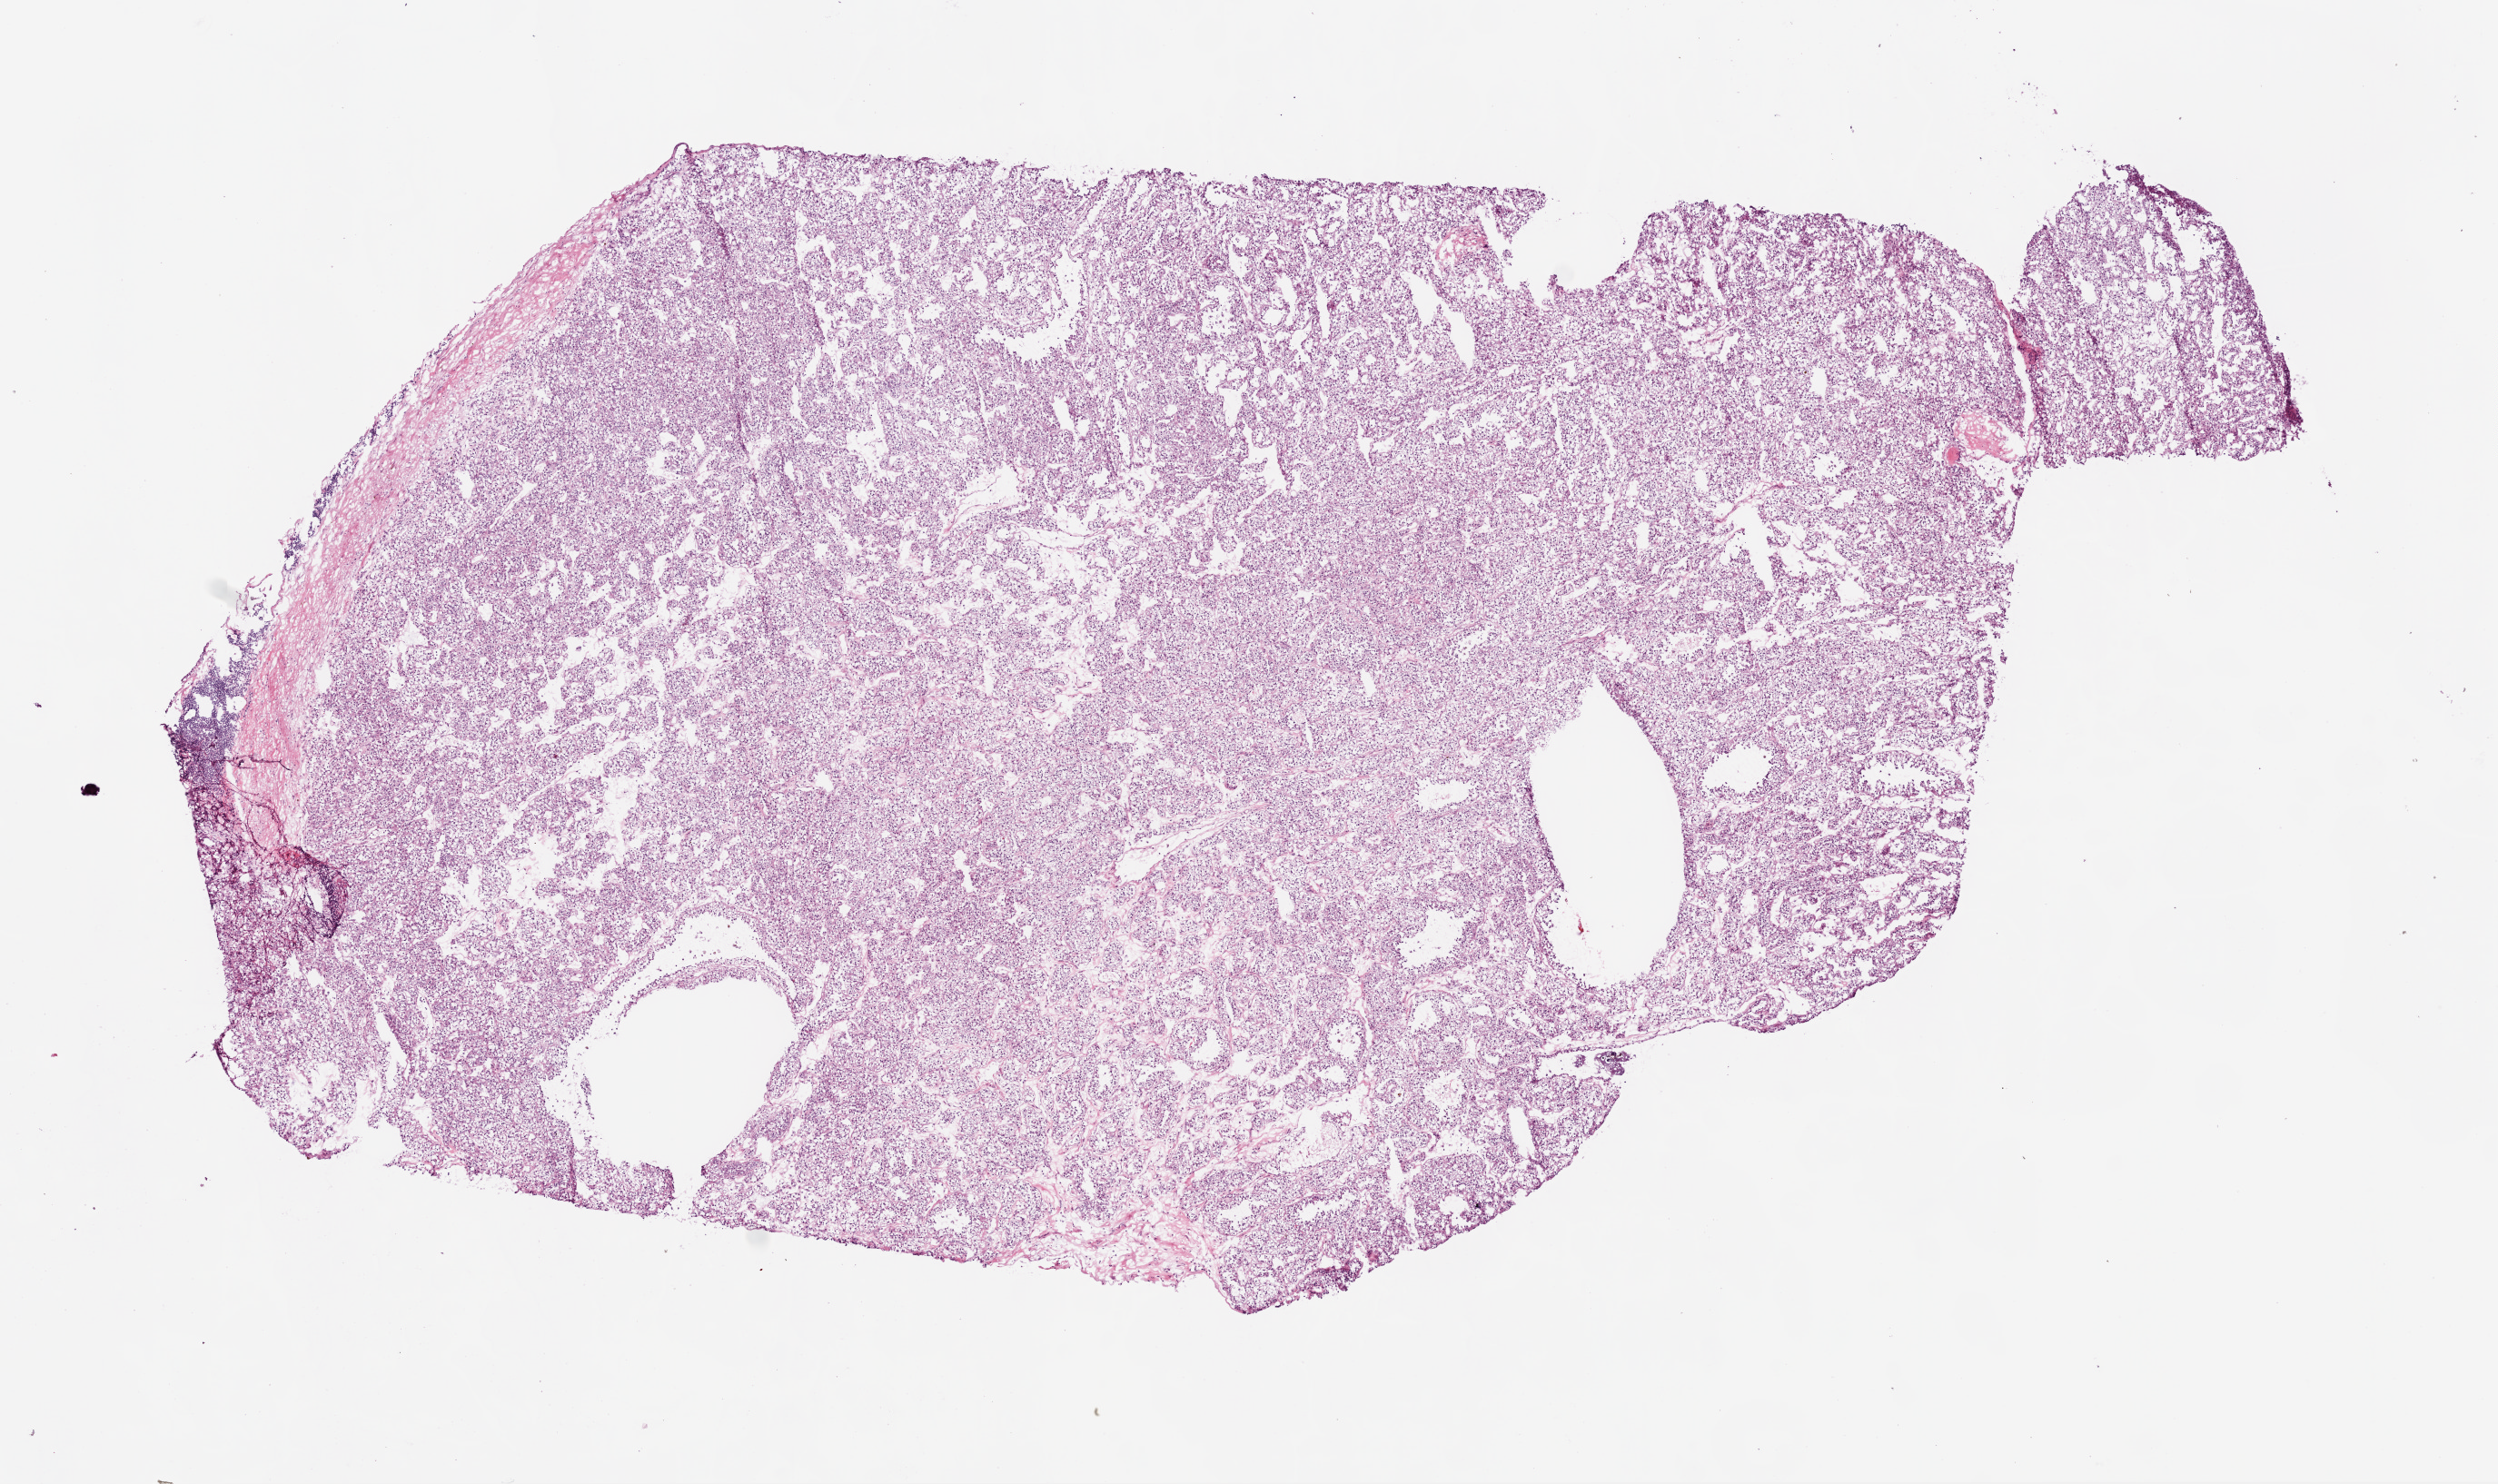
Digitized H&E-stained tissue section (whole slide) — shown as a low-resolution overview of the whole scanned area (about 11.0 x 6.6 mm, from a 20x scan); frozen section from the bottom of the tissue portion; kidney, primary tumour sample. Female patient; age at initial diagnosis 61 years.
Pathologic diagnosis: Clear cell adenocarcinoma, NOS.